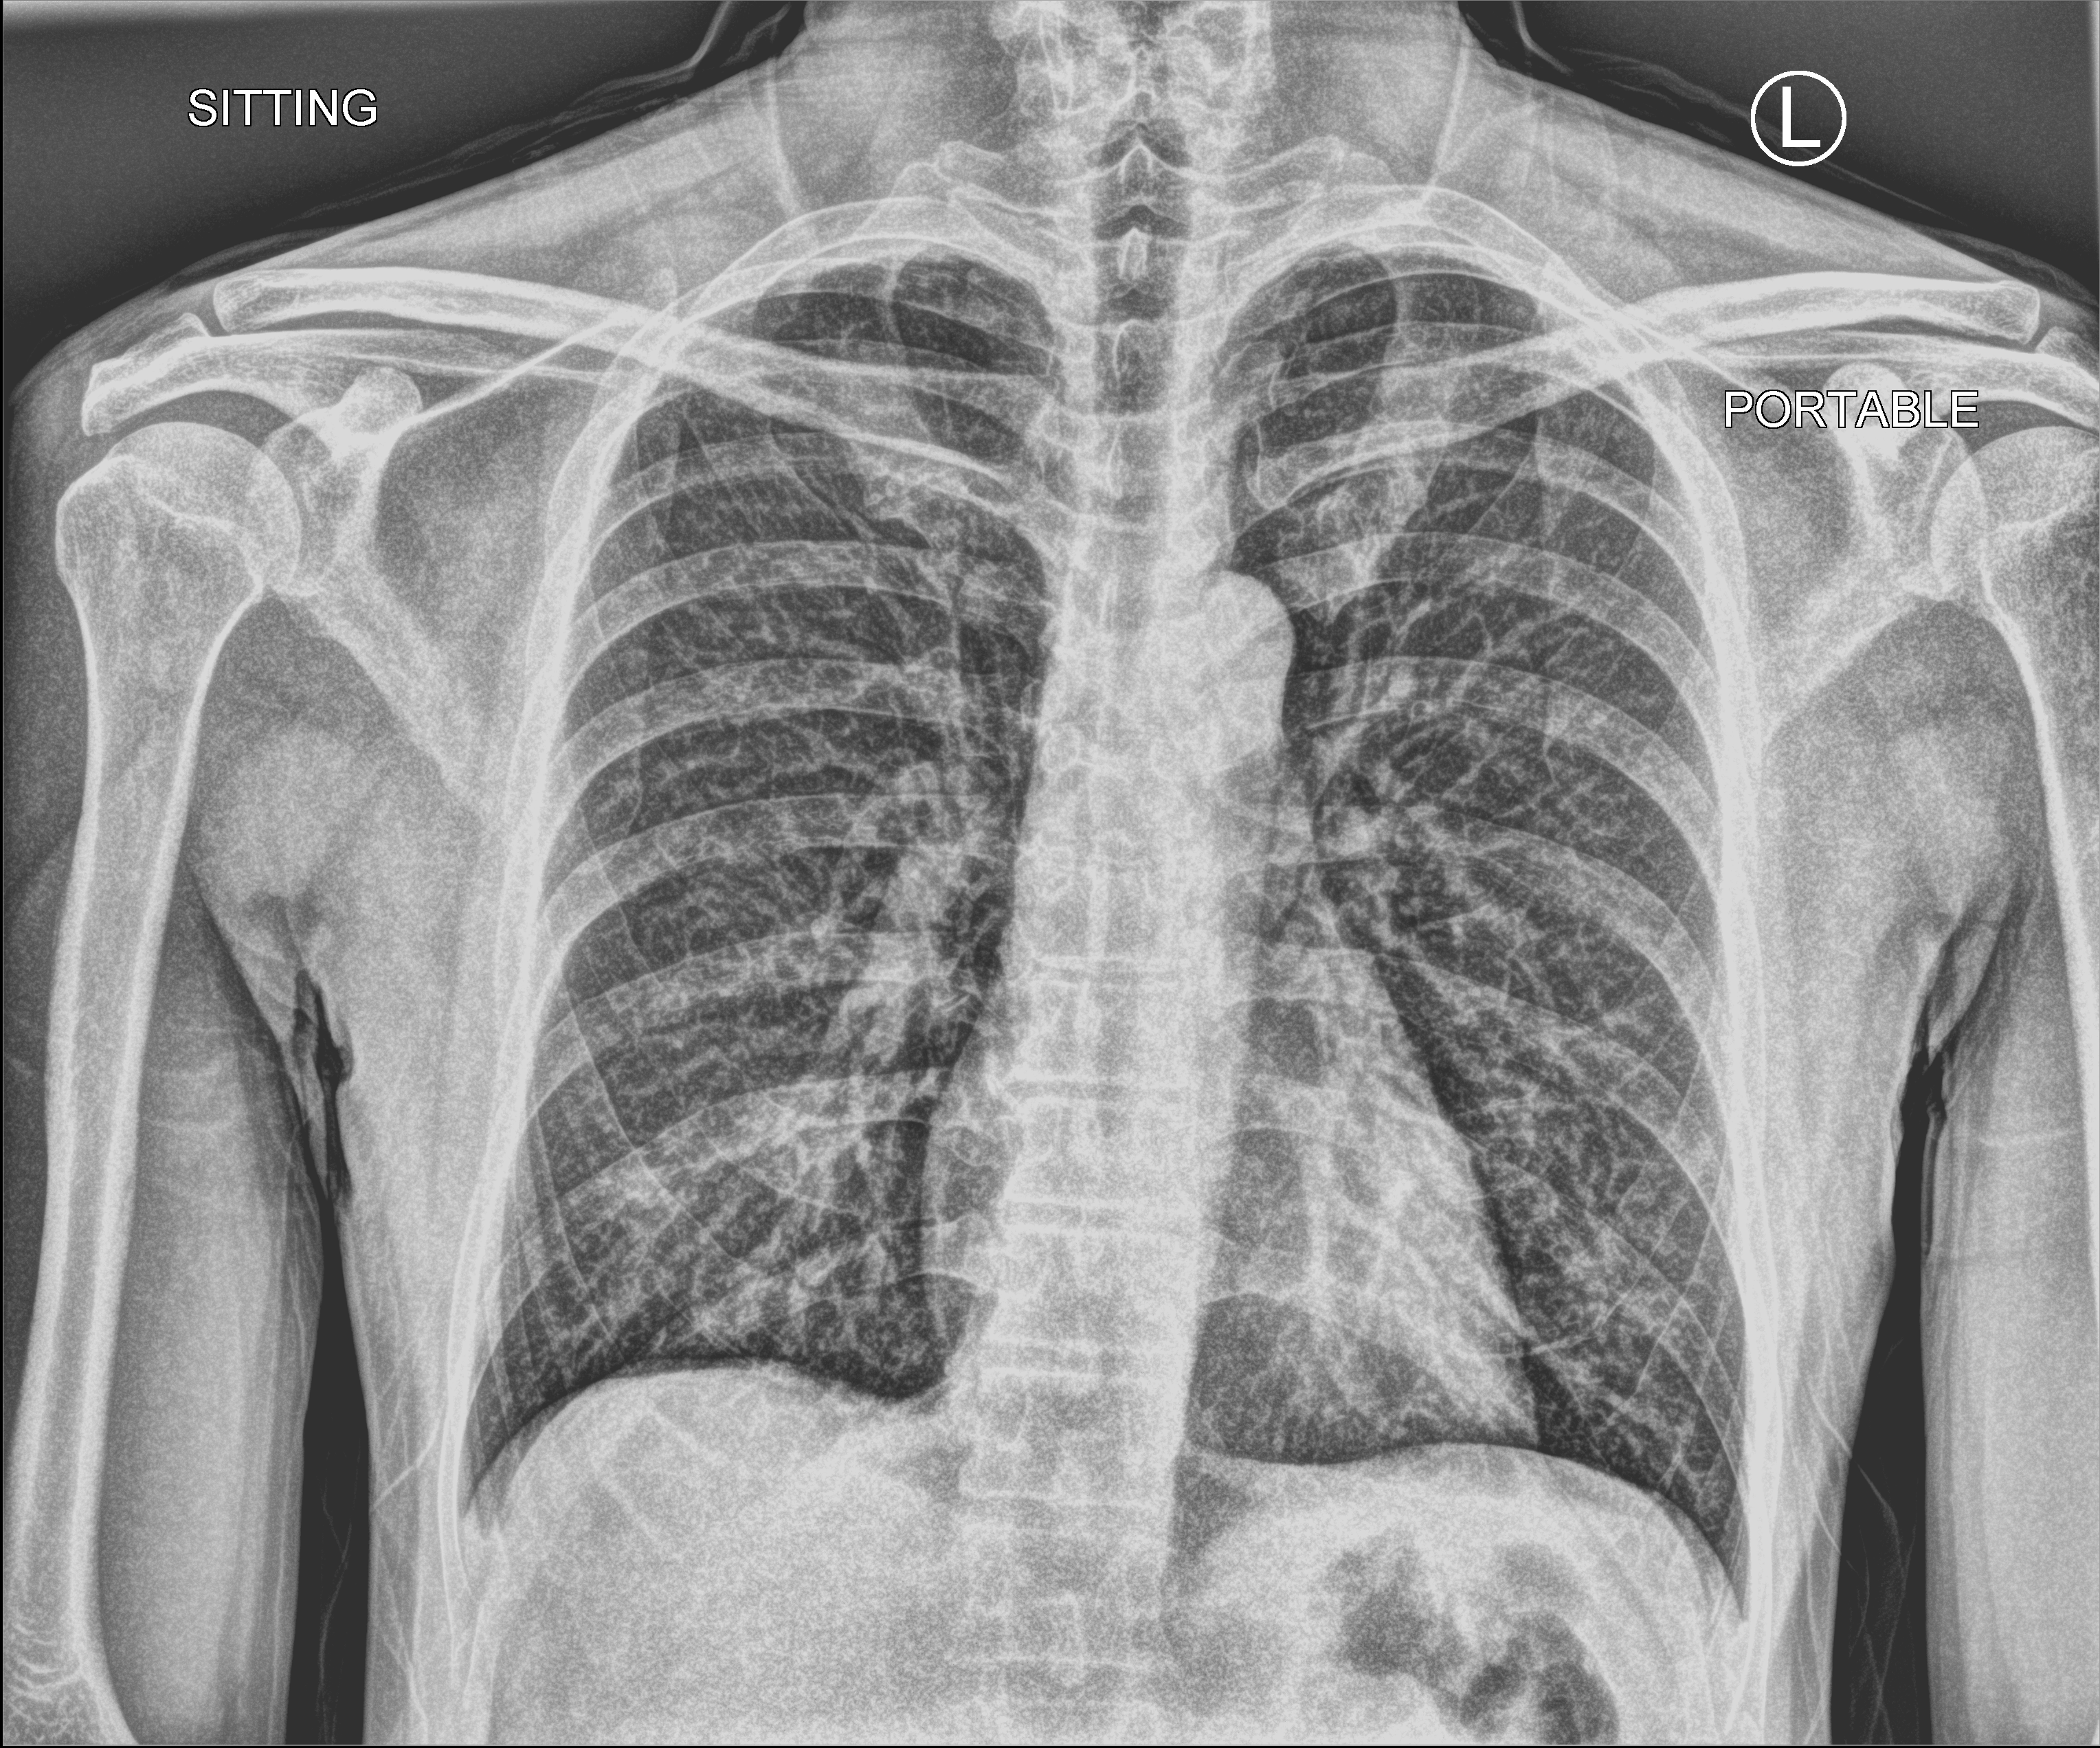
Portable chest radiograph; anteroposterior (AP) projection. Patient hospitalised with COVID-19; male, aged 18–59 years.
Hospital-stay facts (about this admission, not read from this image; timing relative to this image not recorded): admitted to intensive care during this hospital stay: no; length of hospital stay: 1 day.